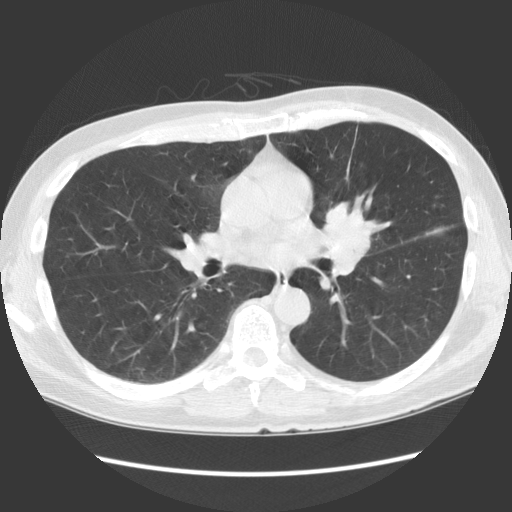
Low-dose screening chest CT, one axial slice; slice 71 of 136 in the series (ordered by position); 140 kVp; lung window (W 1500 / L -600 HU); 512 × 512 image matrix.
Outlined on this slice (manually delineated by an expert):
- lesion 1 (tumor, hilum of left lung): box from (x=323, y=203) to (x=372, y=254) px